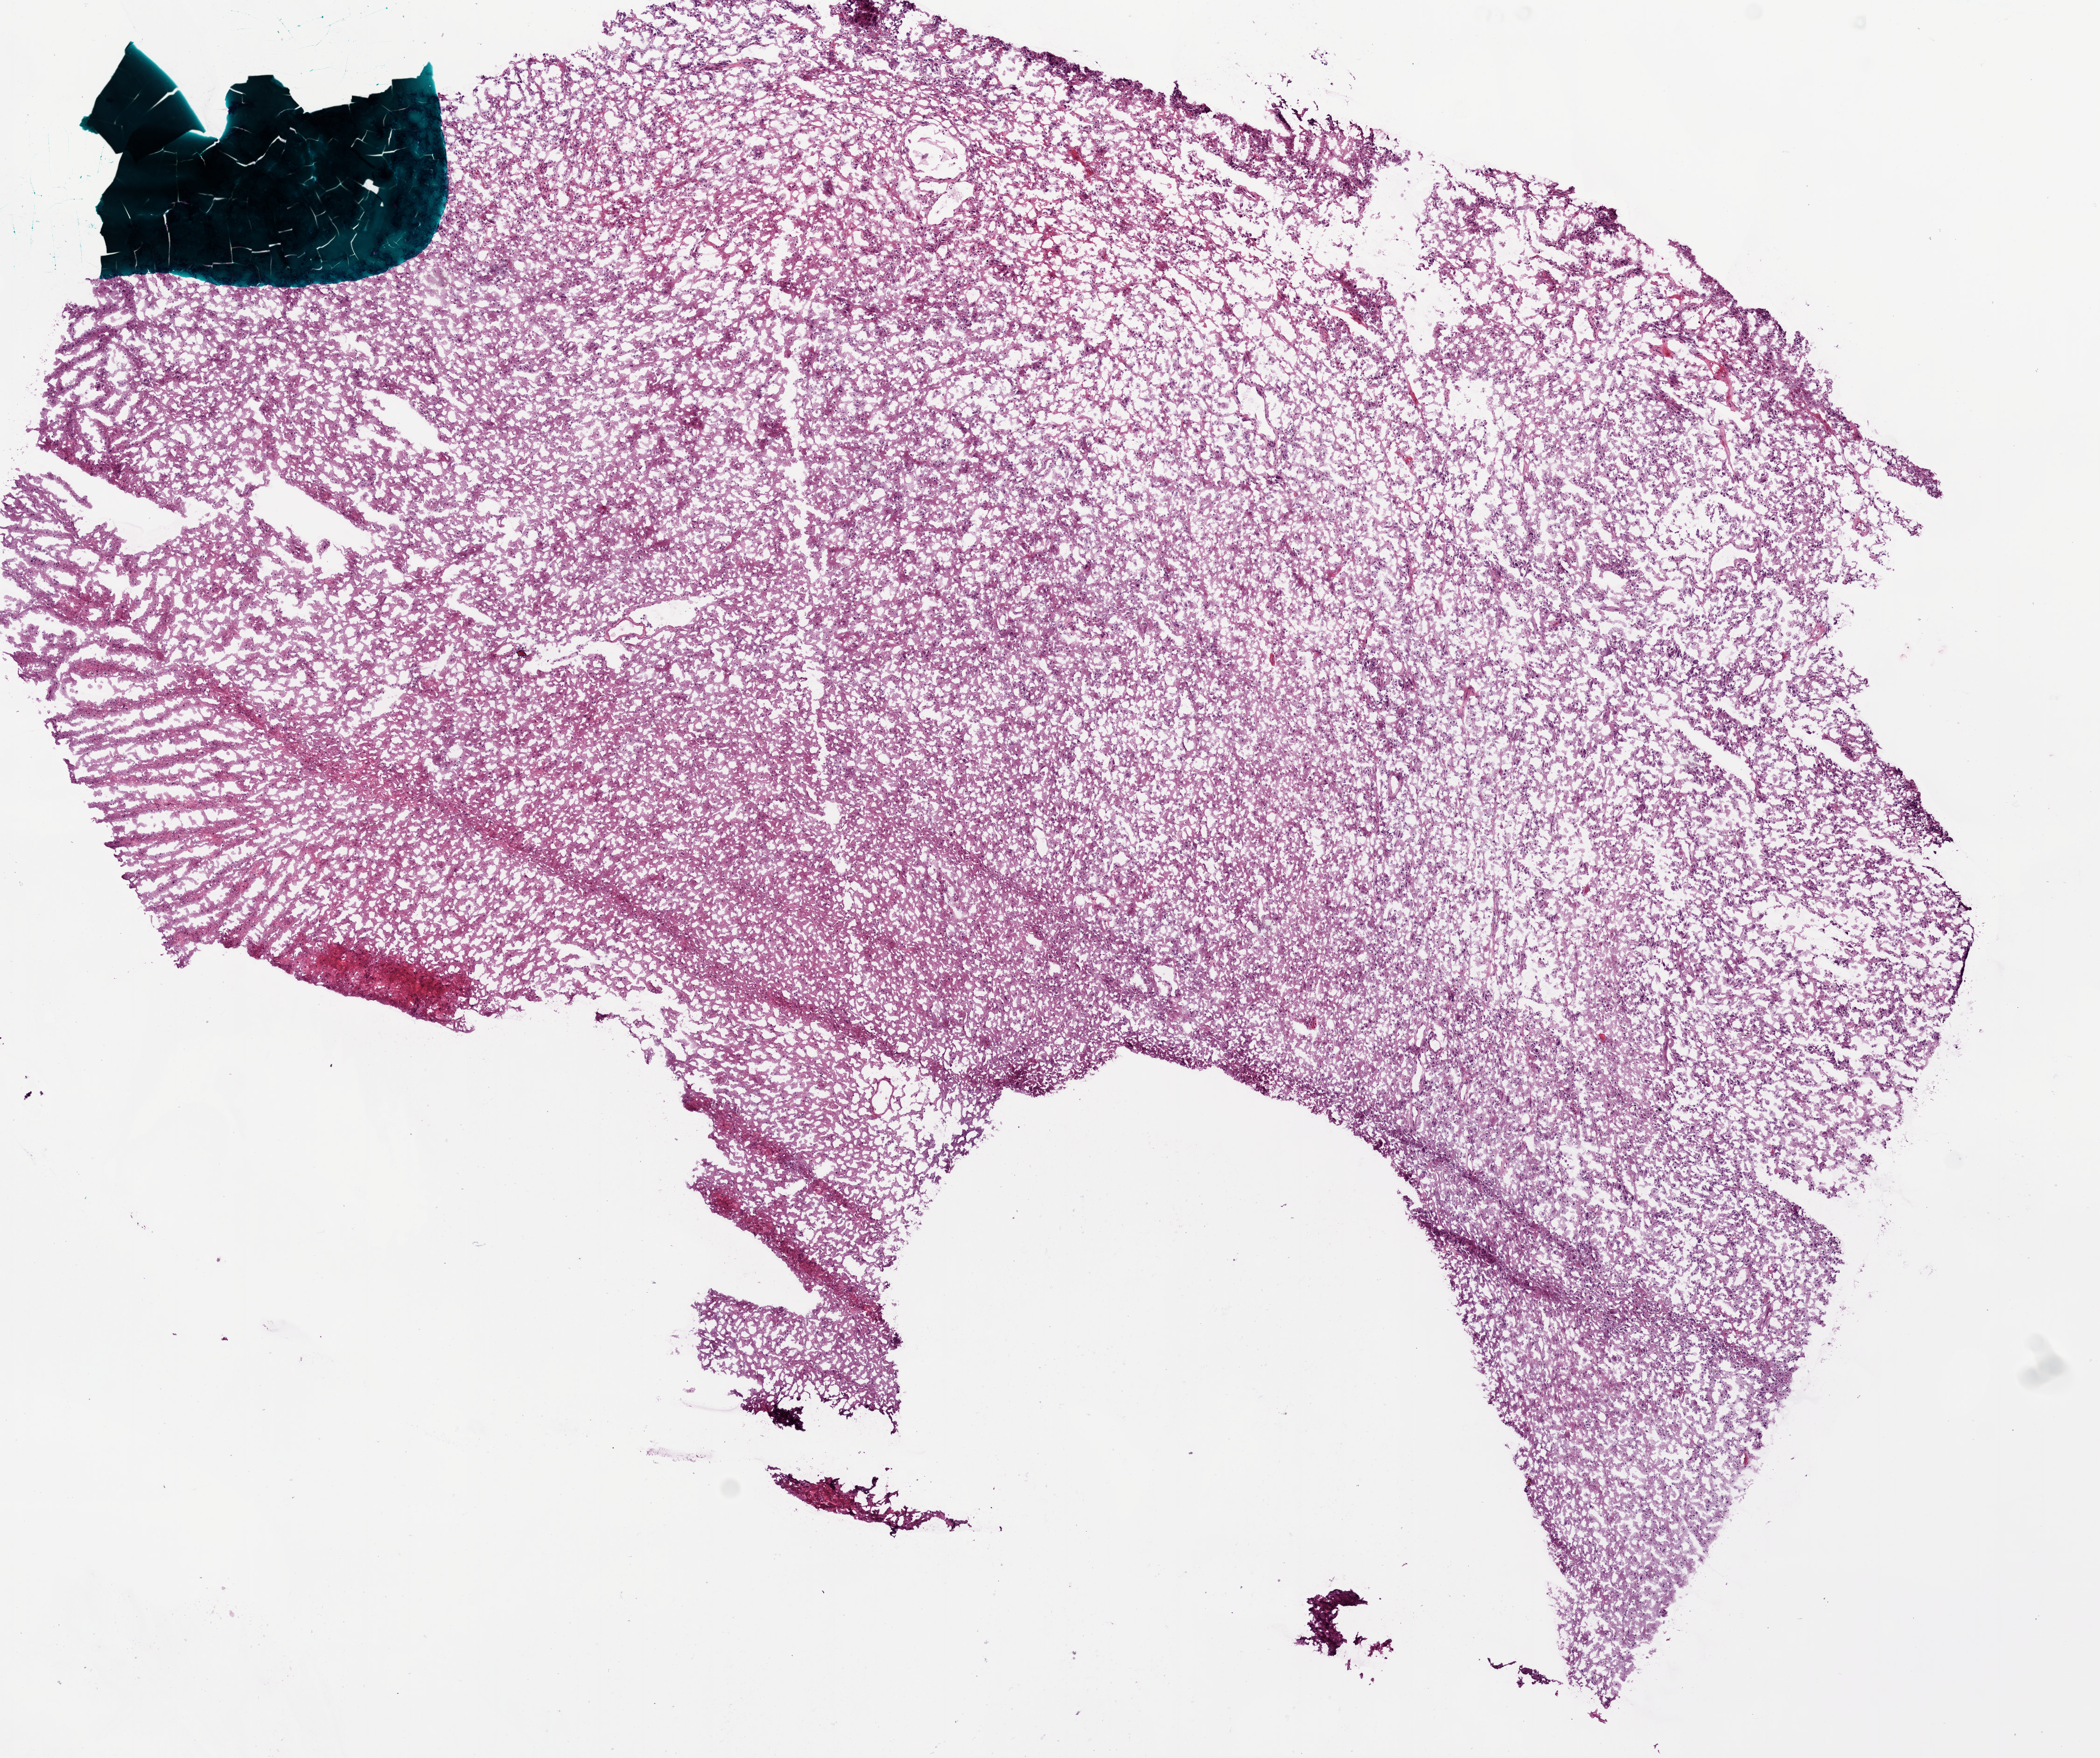
H&E whole-slide image, shown as a low-resolution overview of the whole scanned area (about 9.0 x 7.6 mm), frozen section from the bottom of the tissue portion, primary tumour sample from the brain. Male, age 51 years at initial diagnosis. Slide review estimates, as recorded: tumour cells 100%, tumour nuclei 100%, normal cells 0%, stromal cells 0%, necrosis 0%.
Pathologic diagnosis: Glioblastoma.